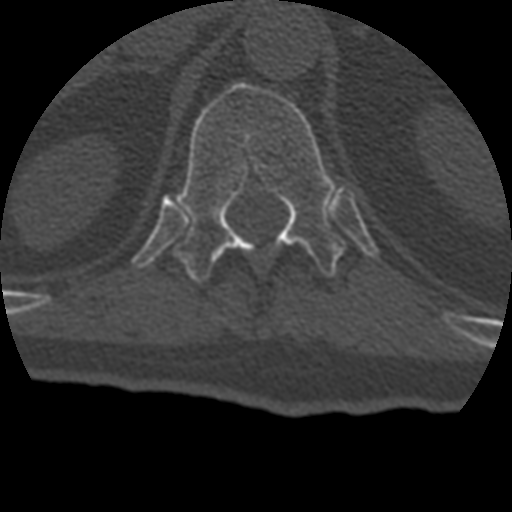
CT including the spine, one axial slice. Slice 177 of 399 in the series (ordered by position). Reconstruction kernel STANDARD. 120 kVp. Bone window (W 1800 / L 400 HU). 512 × 512 image matrix. Patient age 69 years. Case-level facts recorded for this patient, not image findings: primary cancer: prostate.
Outlined on this slice (semi-automatic segmentation, software-assisted and operator-edited):
- T12 vertebra: bounding box [x1, y1, x2, y2] px = [174, 82, 346, 282]